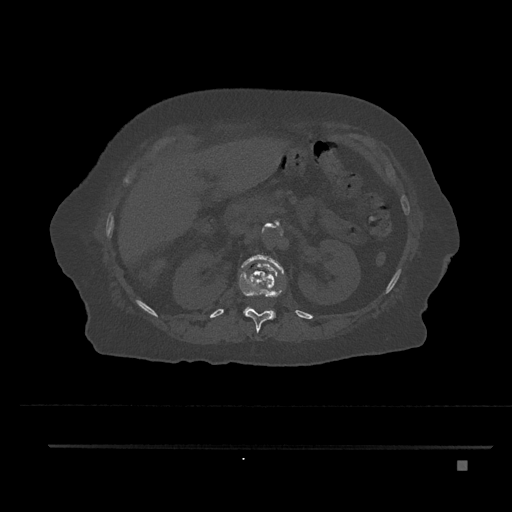
CT including the spine, one axial slice; slice 248 of 797 in the series (ordered by position); 120 kVp; bone window (W 1800 / L 400 HU); 0.5 mm slice thickness; 512 × 512 image matrix, field of view 437 × 437 mm. Female patient, age 76 years. Case-level facts recorded for this patient, not image findings: primary cancer: lung.
Structures marked on this image (semi-automatically segmented with operator editing):
- L1 vertebra: bounding box [x1, y1, x2, y2] px = [242, 254, 285, 317]
- T12 vertebra: [239, 270, 284, 332]